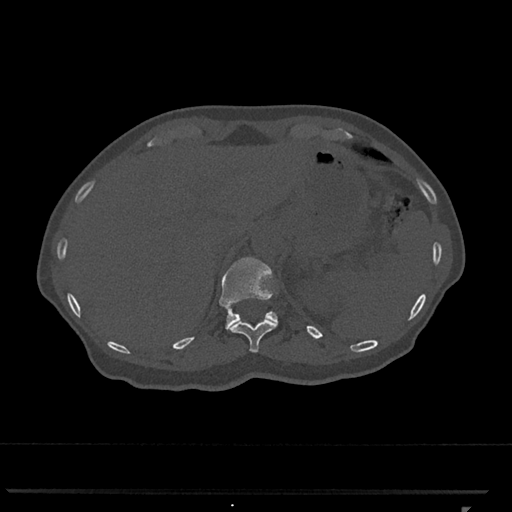
CT including the spine, one axial slice; position 494 of 793 along the scan axis; 120 kVp; bone window (W 1800 / L 400 HU); 0.5 mm slice thickness; 512 × 512 image matrix, field of view 380 × 380 mm. Patient: female, 62 years. Case-level facts recorded for this patient, not image findings: primary cancer: renal.
Structures marked on this image (semi-automatic segmentation, software-assisted and operator-edited):
- T11 vertebra: bounding box [x1, y1, x2, y2] px = [228, 319, 278, 353]
- T12 vertebra: [219, 257, 278, 330]